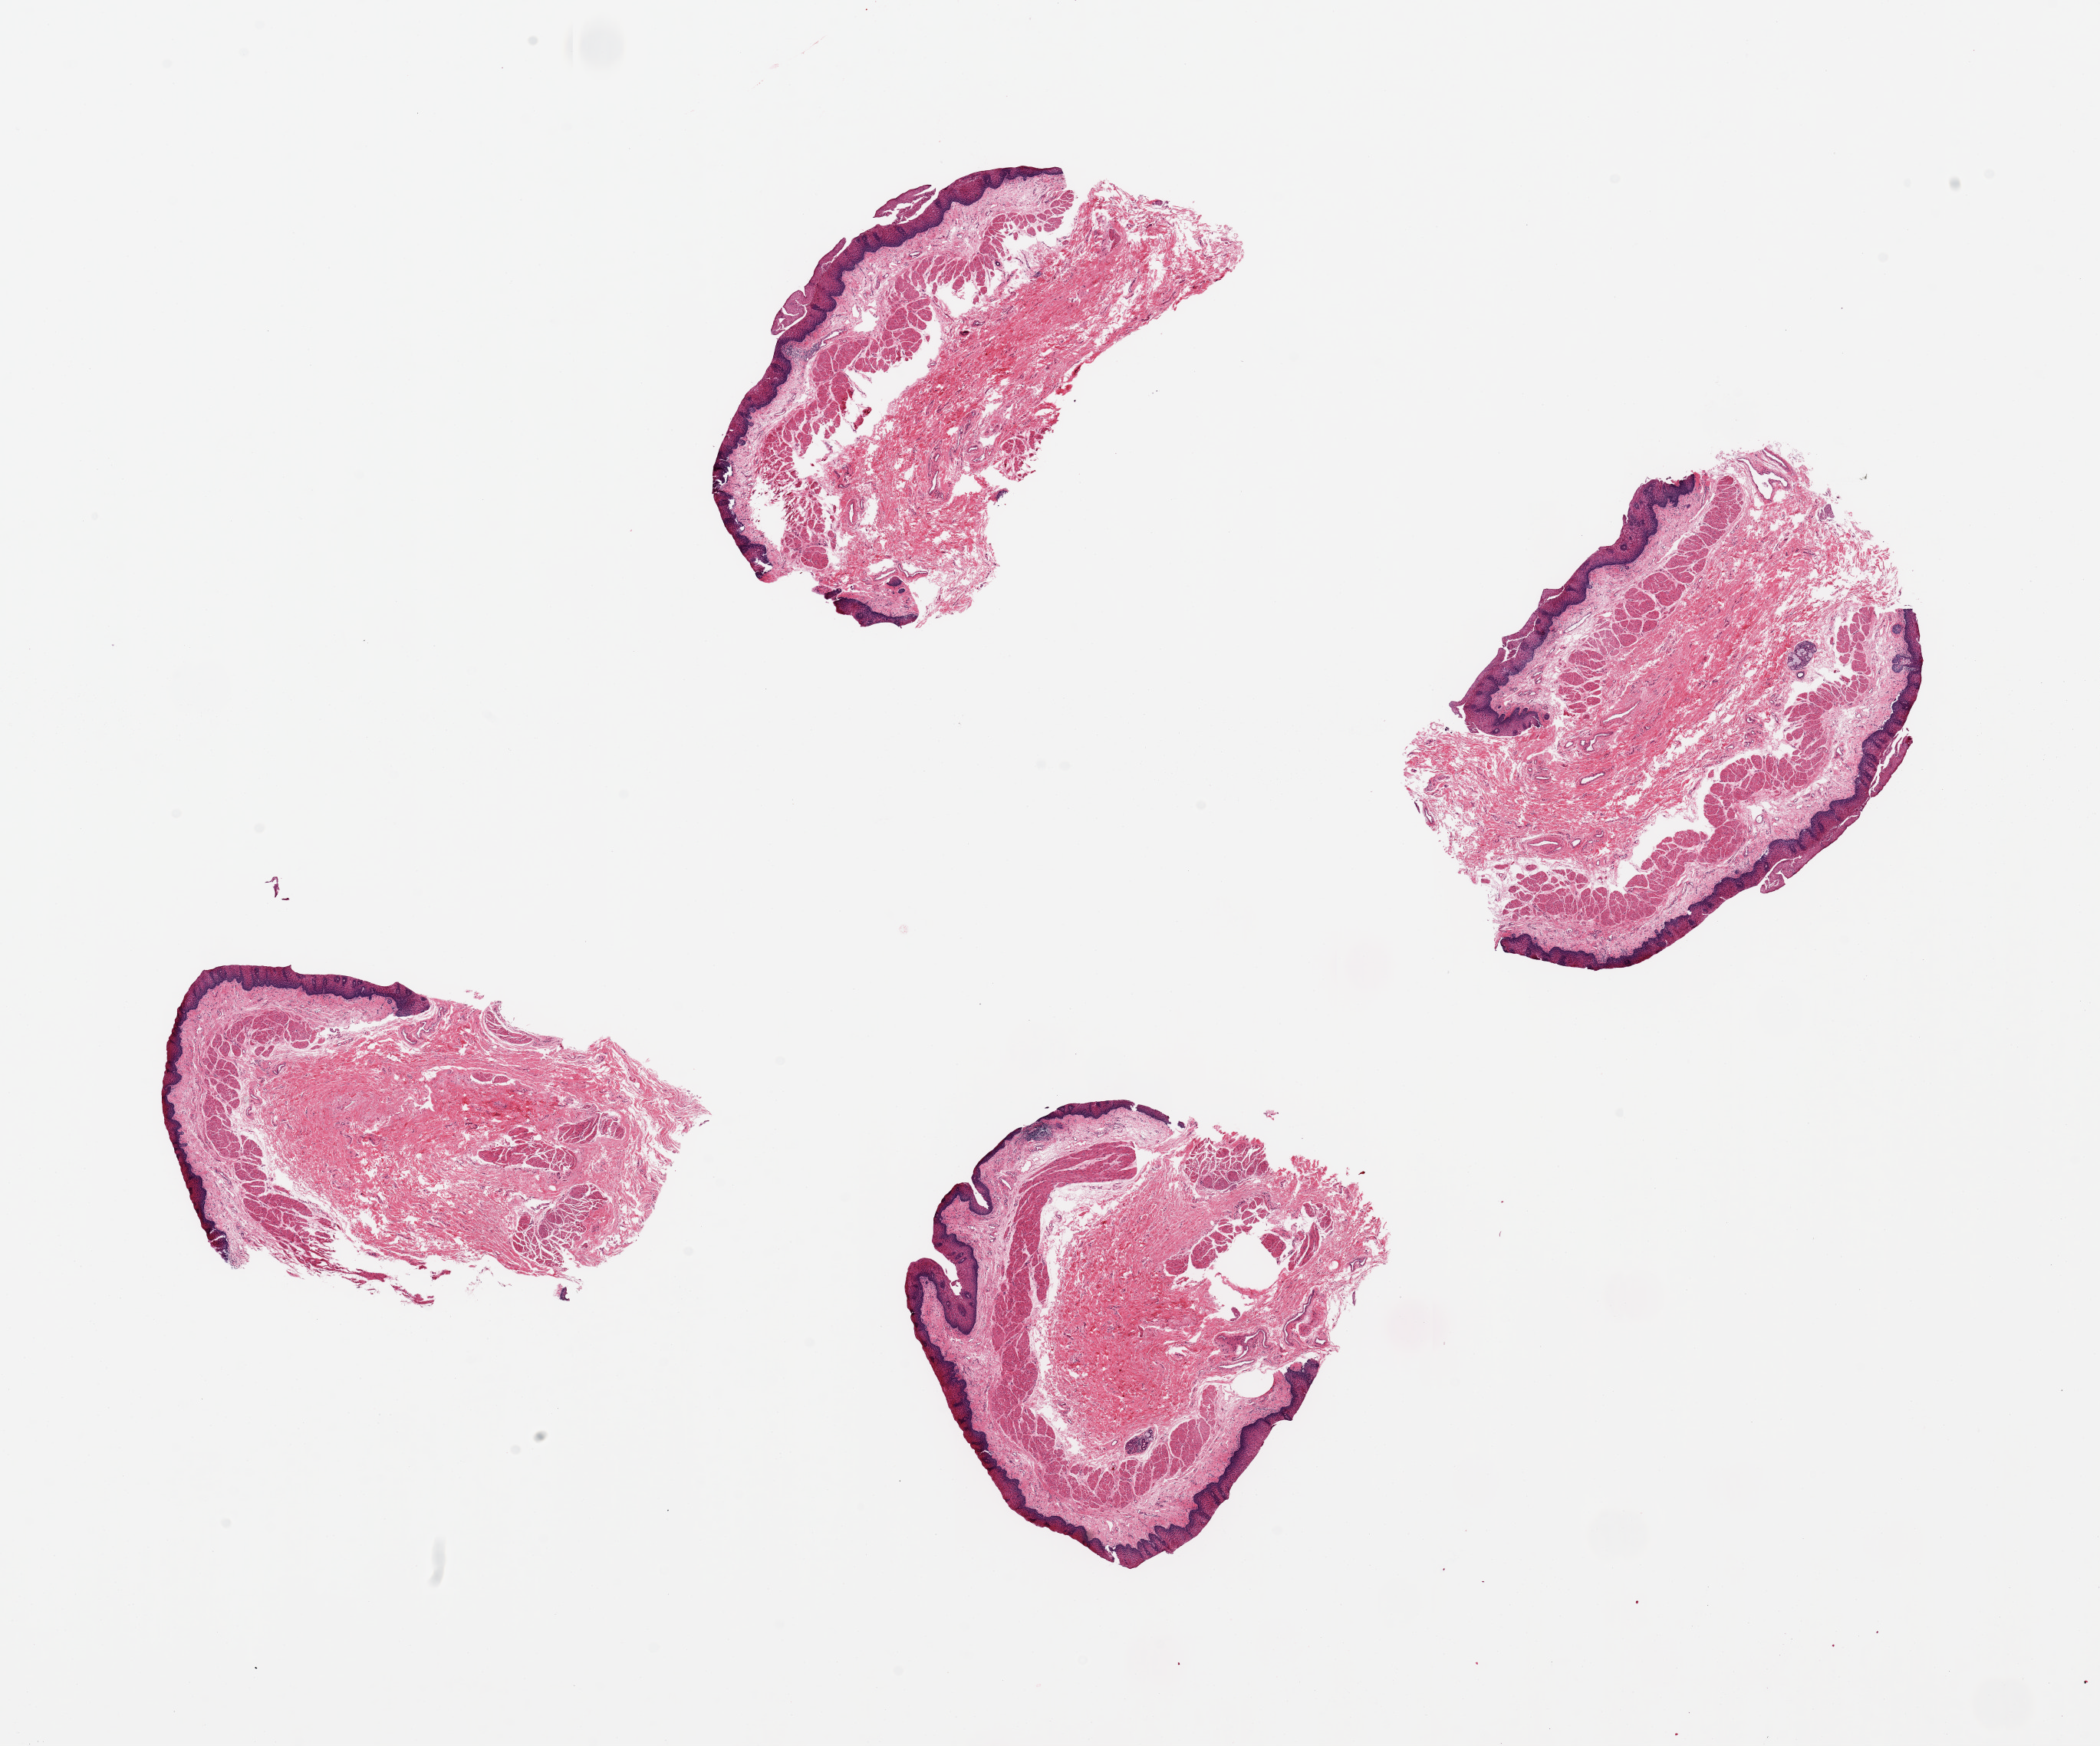
Digitized hematoxylin and eosin (H&E)-stained section — shown as a low-resolution overview of the whole scanned area (about 21.7 x 18.0 mm). PAXgene-fixed paraffin-embedded (PFPE) section. Target tissue: esophageal mucous membrane. Donor tissue sample.
Pathologist's review note for this sample: 4 pieces, up to 5.5 x 3mm; well sampled.